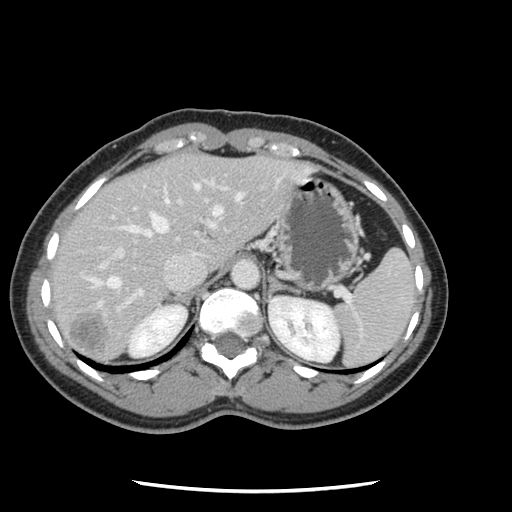
Contrast-enhanced abdominal CT, one axial slice. Slice 88 of 134 in the series (ordered by position). 120 kVp. Soft-tissue window (W 400 / L 40 HU). 512 × 512 image matrix, field of view 330 × 330 mm. Female patient, age 43 years. Case-level facts recorded for this patient, not image findings: diagnosis: colorectal cancer liver metastases, imaged before liver resection; multiple liver metastases: yes; largest metastasis: 3.4 cm; disease in both lobes: yes.
Outlined on this slice (manually delineated by an expert):
- hepatic veins: box from (x=88, y=183) to (x=242, y=305) px
- liver: (x=52, y=153)–(x=310, y=363)
- planned liver remnant (the part of the liver to remain after resection): (x=52, y=157)–(x=191, y=309)
- portal vein (with intrahepatic branches): (x=80, y=180)–(x=227, y=313)
- liver metastasis: (x=70, y=314)–(x=107, y=350)